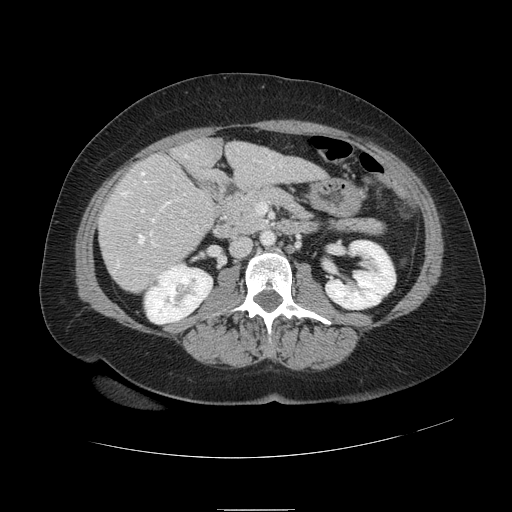
Contrast-enhanced abdominal CT, one axial slice; position 35 of 121 along the scan axis; 120 kVp; intravenous contrast given; soft-tissue window (W 400 / L 40 HU); 512 × 512 image matrix, field of view 400 × 400 mm. Female patient, age 52 years. From the clinical record (not read from this slice): diagnosis: colorectal cancer liver metastases, imaged before liver resection; multiple liver metastases: yes; largest metastasis: 6.3 cm; disease in both lobes: no.
Structures marked on this image (expert manual segmentation):
- hepatic veins: bounding box [x1, y1, x2, y2] px = [117, 155, 188, 267]
- liver: [100, 139, 323, 292]
- planned liver remnant (the part of the liver to remain after resection): [175, 139, 323, 184]
- portal vein (with intrahepatic branches): [141, 209, 172, 217]